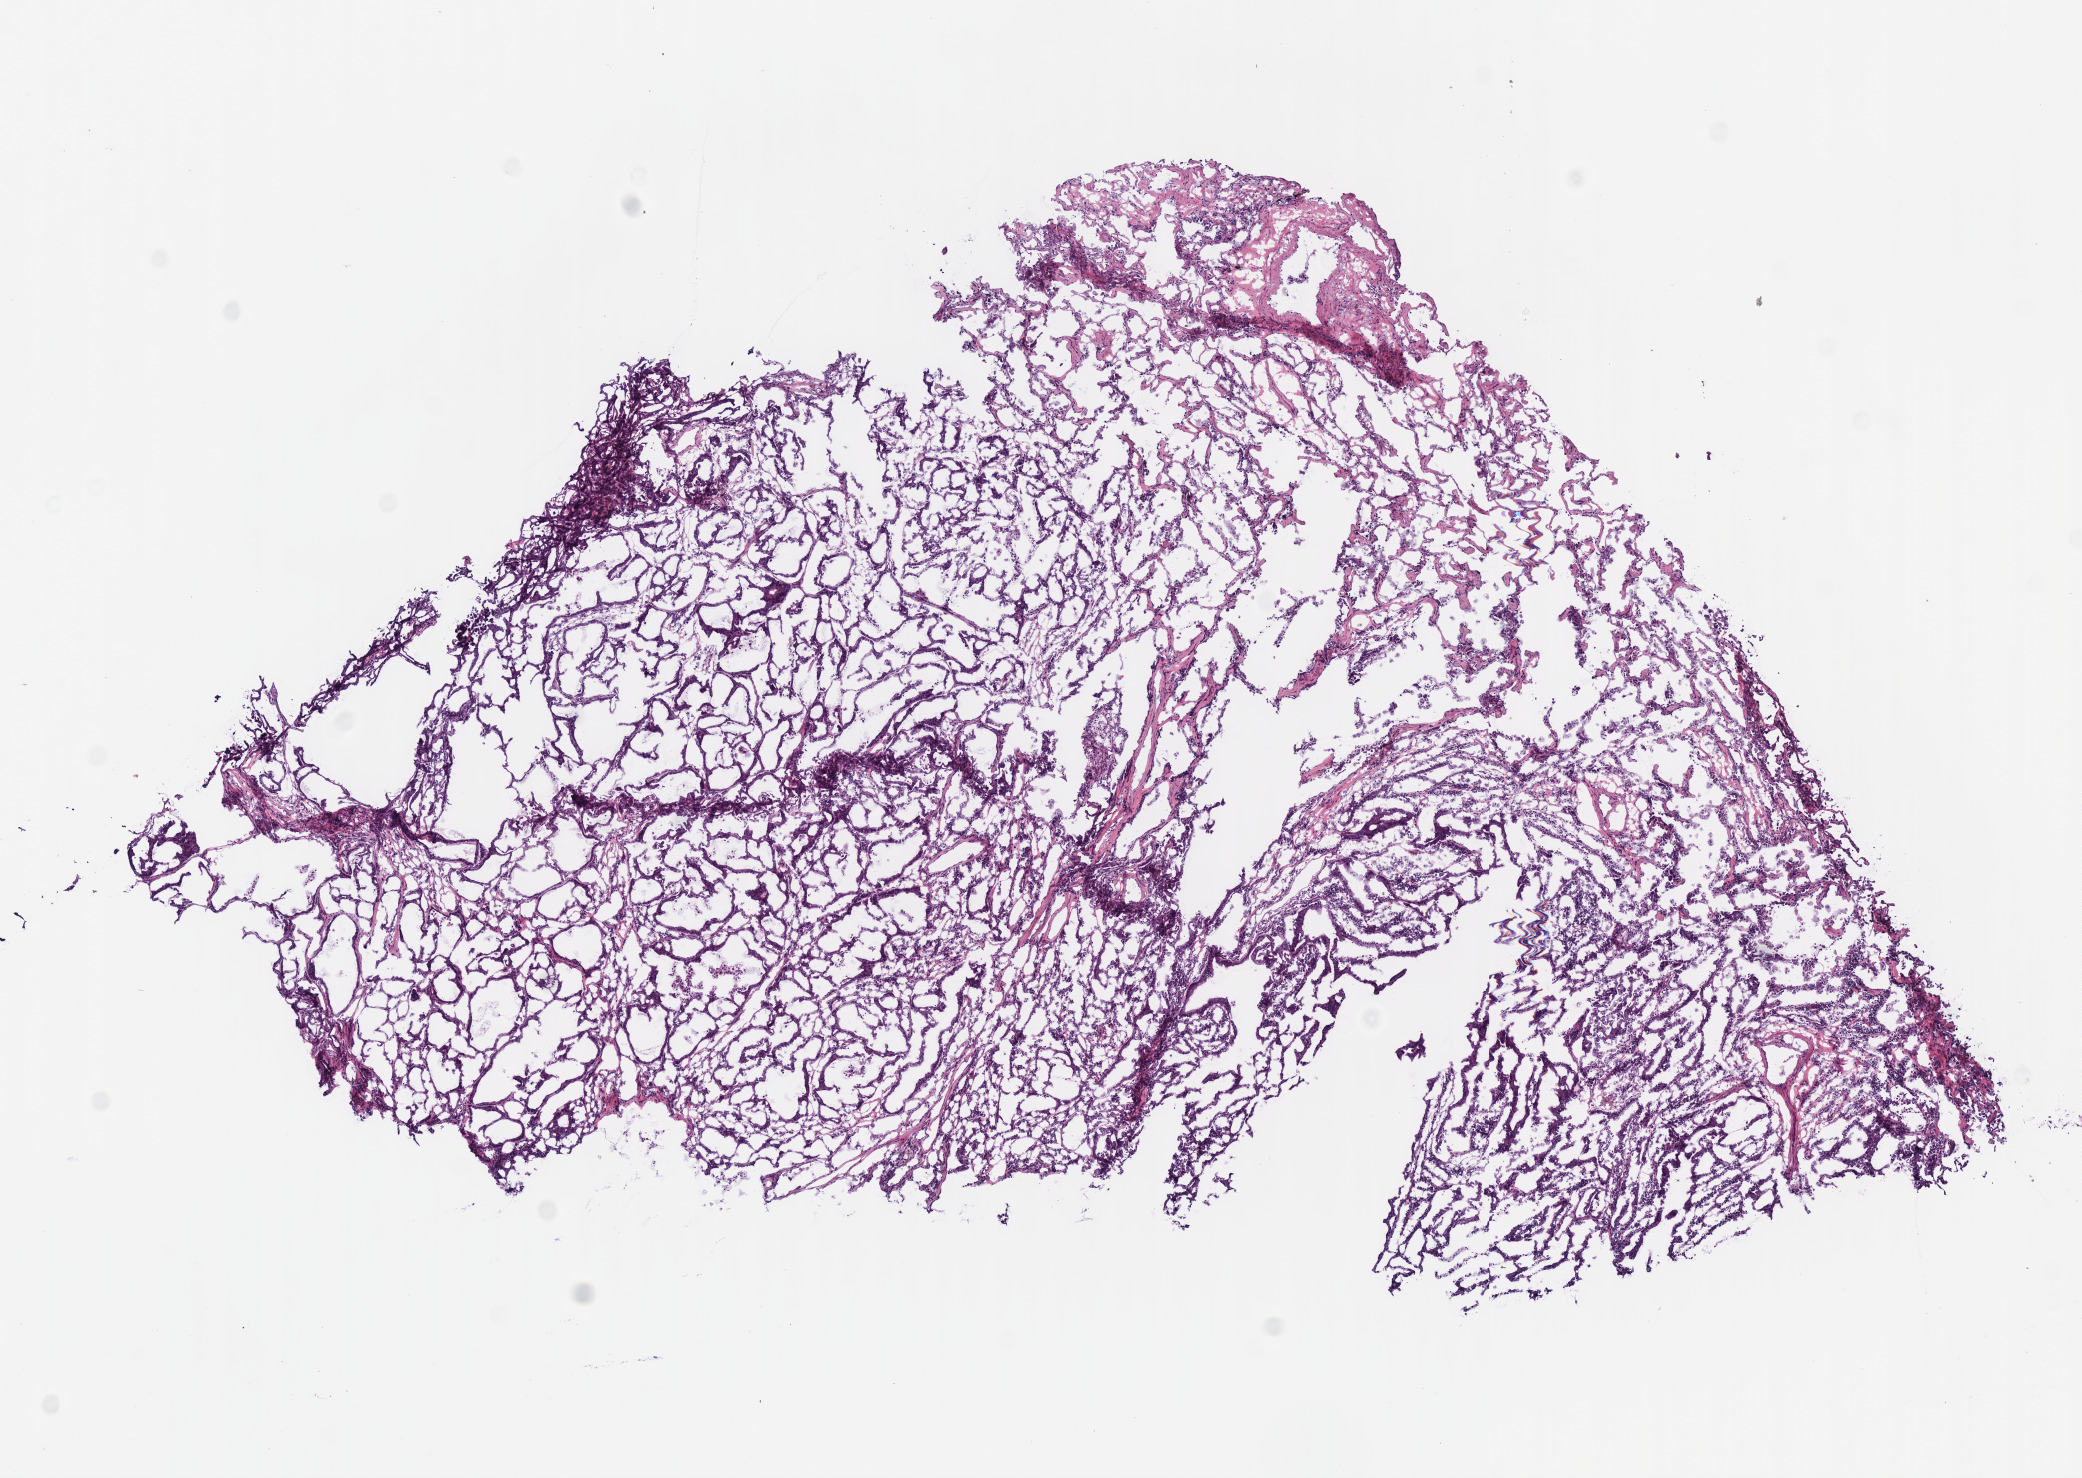
H&E whole-slide image — a low-resolution overview of the entire scanned area, about 8.2 x 5.8 mm; frozen section; sample: primary tumour, lung. Female patient; age at initial diagnosis 51 years. Slide review estimates, as recorded: tumour cells 78%, tumour nuclei 55%, normal cells 22%, stromal cells 0%, necrosis 0%. Infiltration values recorded for this section: lymphocyte infiltration 10%, monocyte infiltration 12%, neutrophil infiltration 10%.
- histologic diagnosis: Bronchiolo-alveolar carcinoma, non-mucinous (upper lobe, lung)
- TNM: T4 N0 M0
- AJCC pathologic stage: IIIB